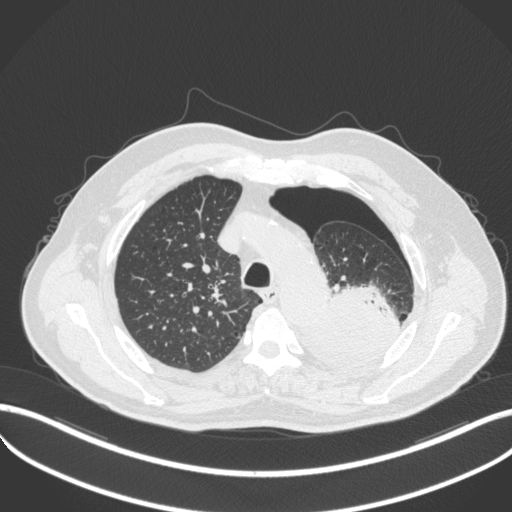
Chest CT, one axial slice; 120 kVp; lung window (W 1500 / L -600 HU); 1 mm slice thickness; 512 × 512 image matrix, field of view 400 × 400 mm. Patient: male, 76 years. From the clinical record (not read from this slice): clinical TNM (as recorded): T3 N0 M1b.
Outlined on this slice (bounding box drawn by a radiologist):
- lung tumour (recorded histology: adenocarcinoma): bounding box [x1, y1, x2, y2] px = [298, 278, 401, 369]